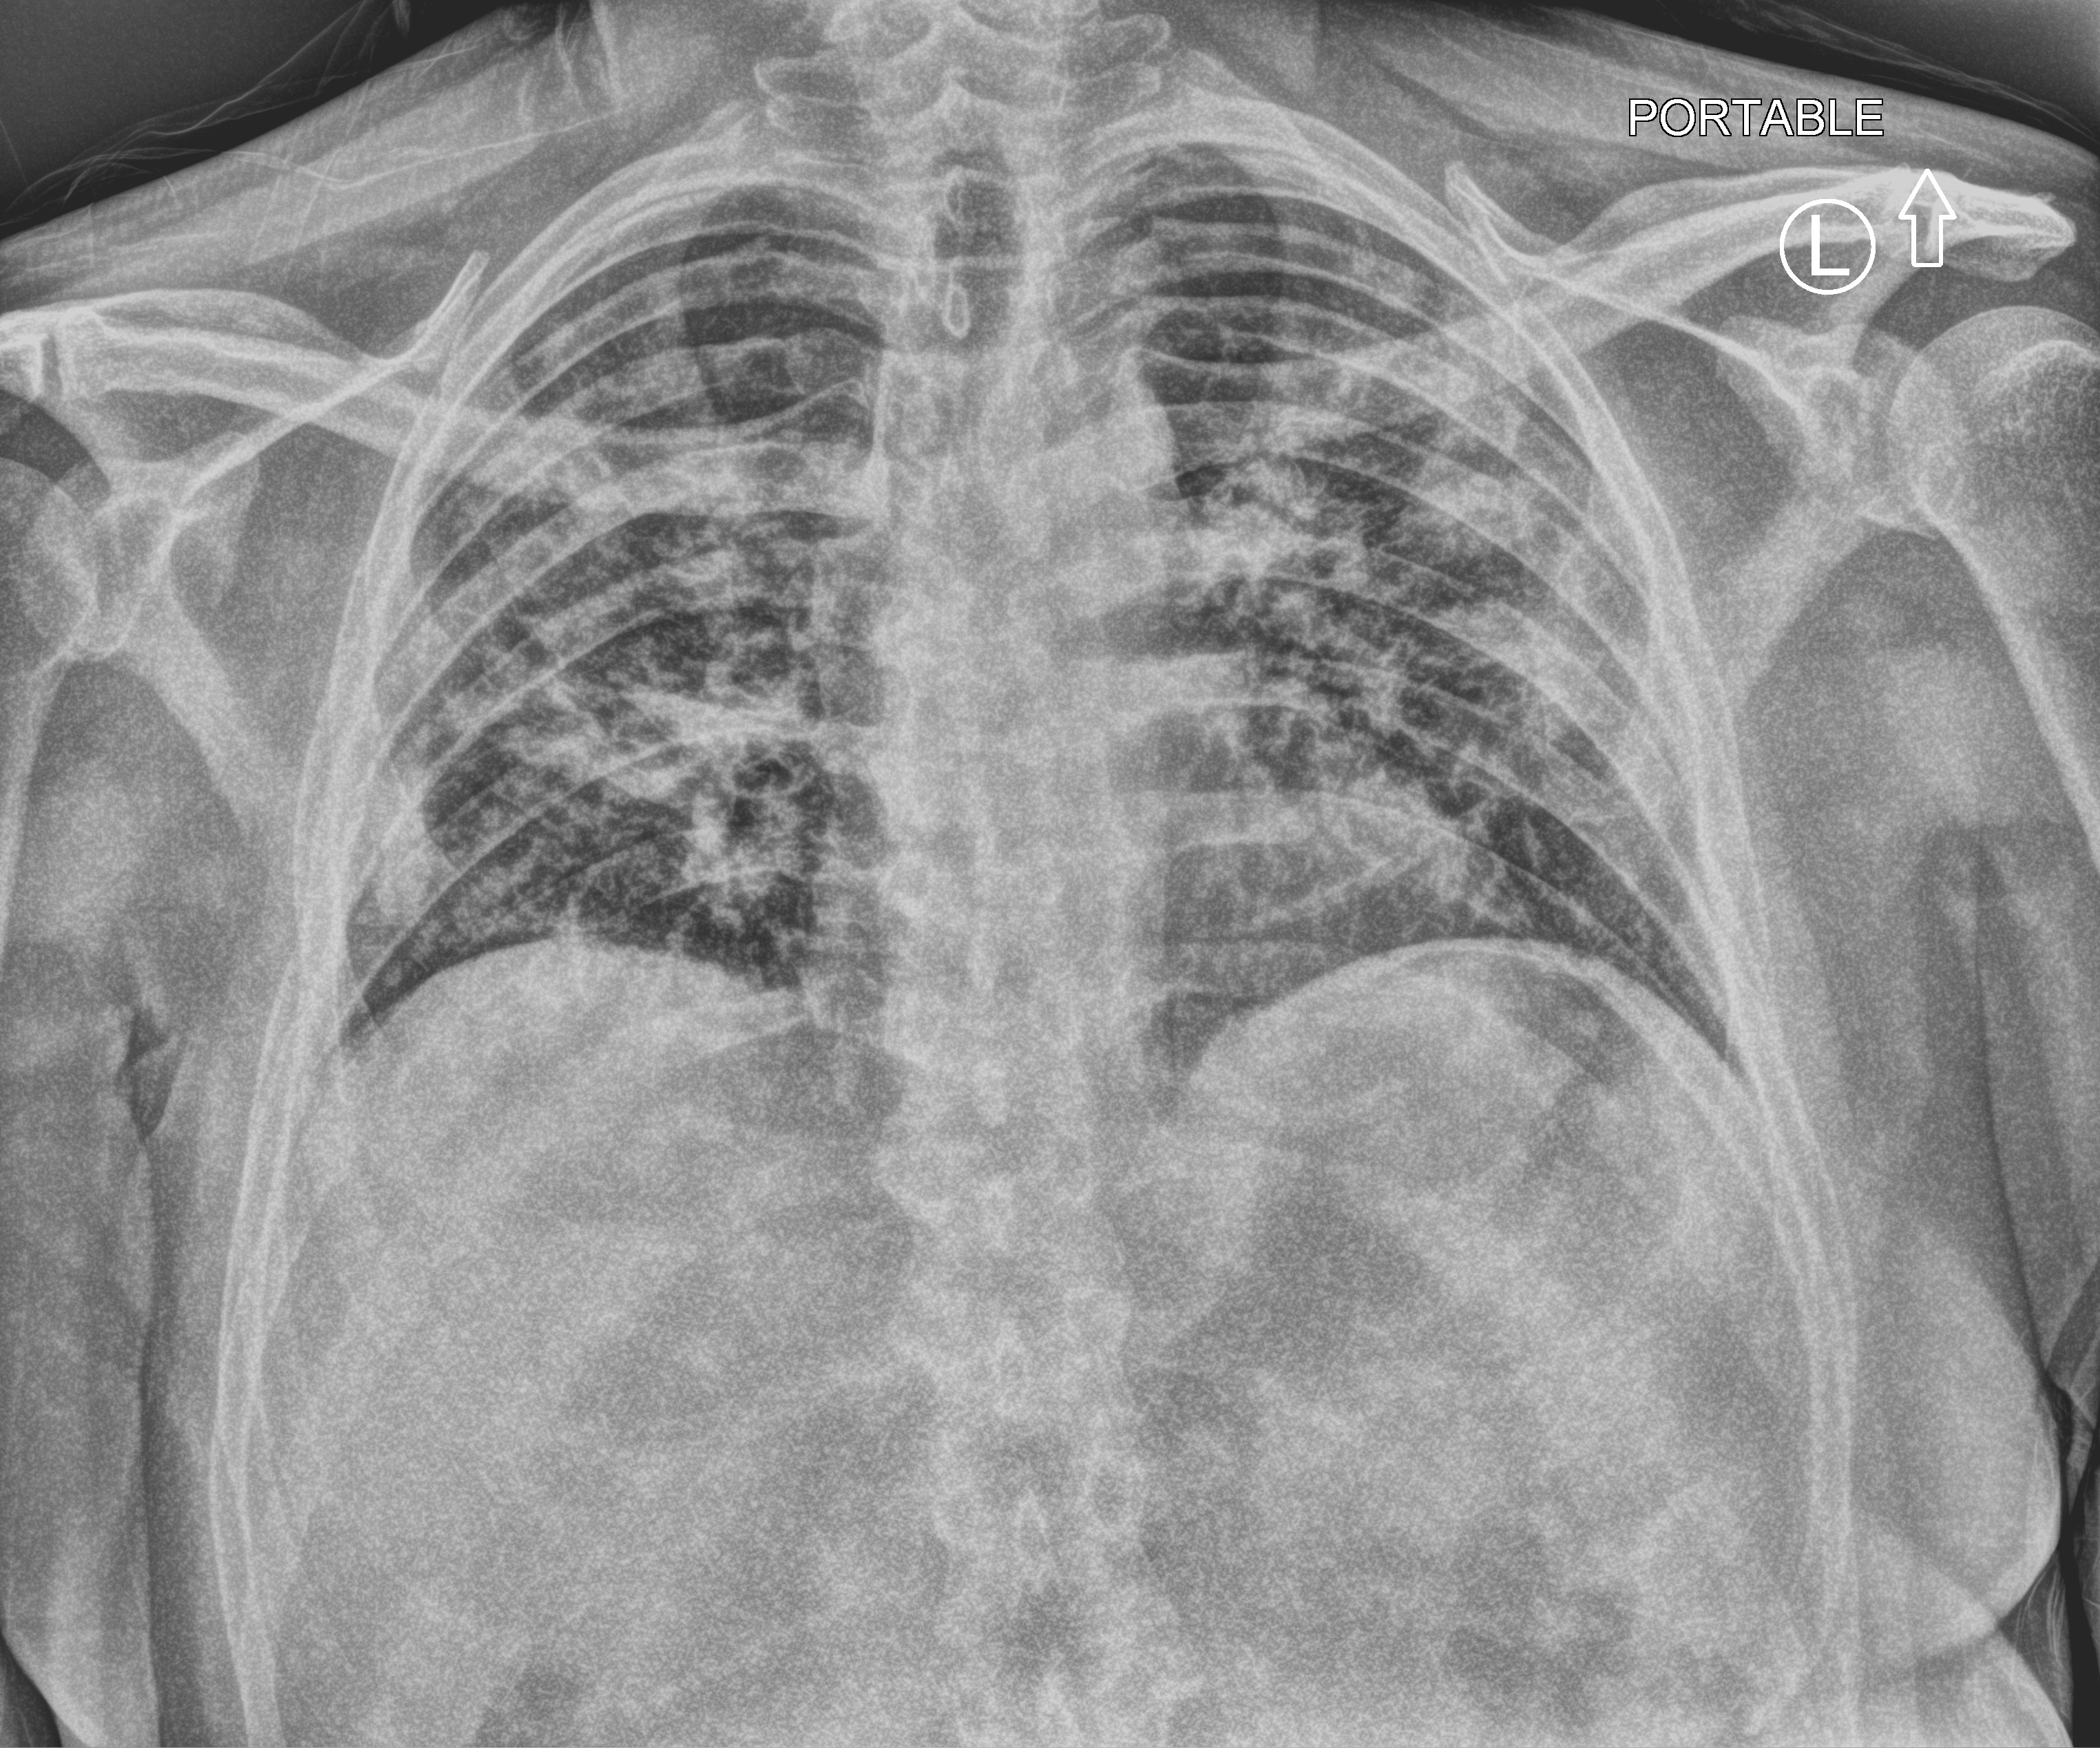
Chest X-ray (portable), anteroposterior (AP) projection. Patient hospitalised with COVID-19; male, aged 18–59 years.
Admission-level facts for this patient (not findings on this image; timing relative to this image not recorded):
- admitted to intensive care during this hospital stay: no
- smoking status (admission record): never
- diabetes (admission record): yes